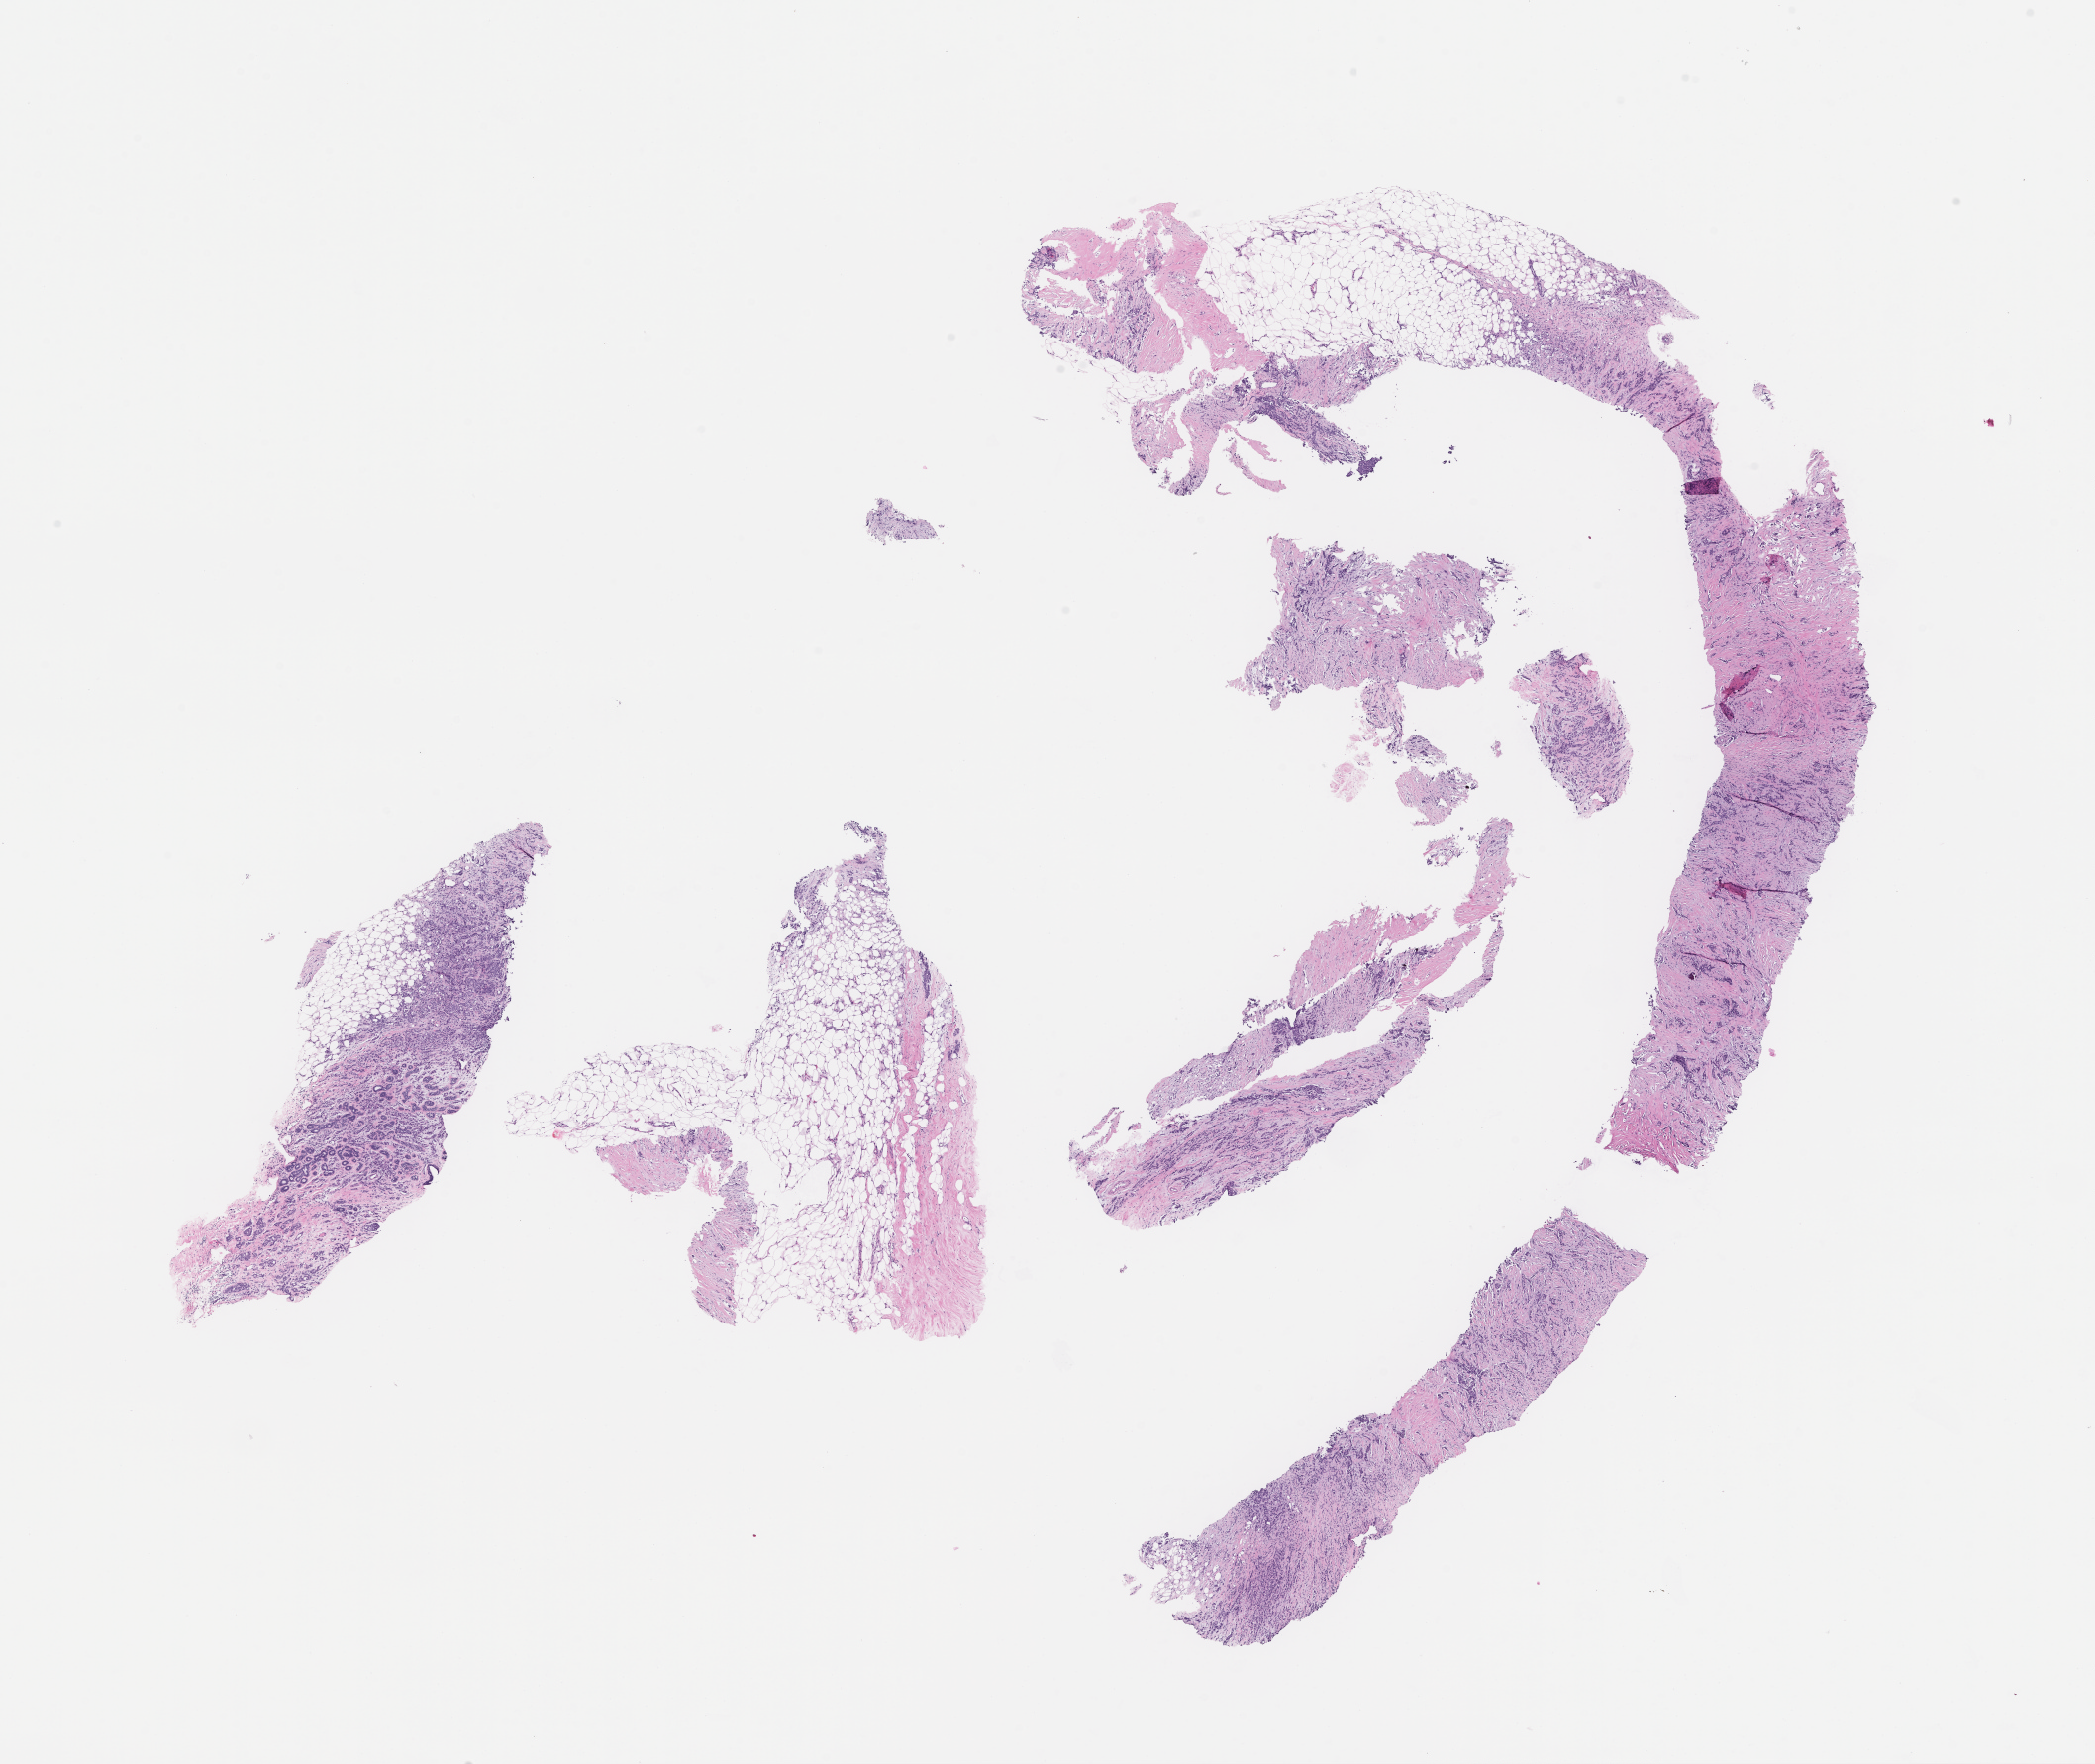
H&E whole-slide image, shown as a low-resolution overview of the whole scanned area (about 17.1 x 14.4 mm). Formalin-fixed, paraffin-embedded (FFPE) tissue. Tissue site: breast. Specimen time point: archival tissue. Patient sex: female.
* this section: primary tumor
* diagnosis: Invasive Breast Carcinoma